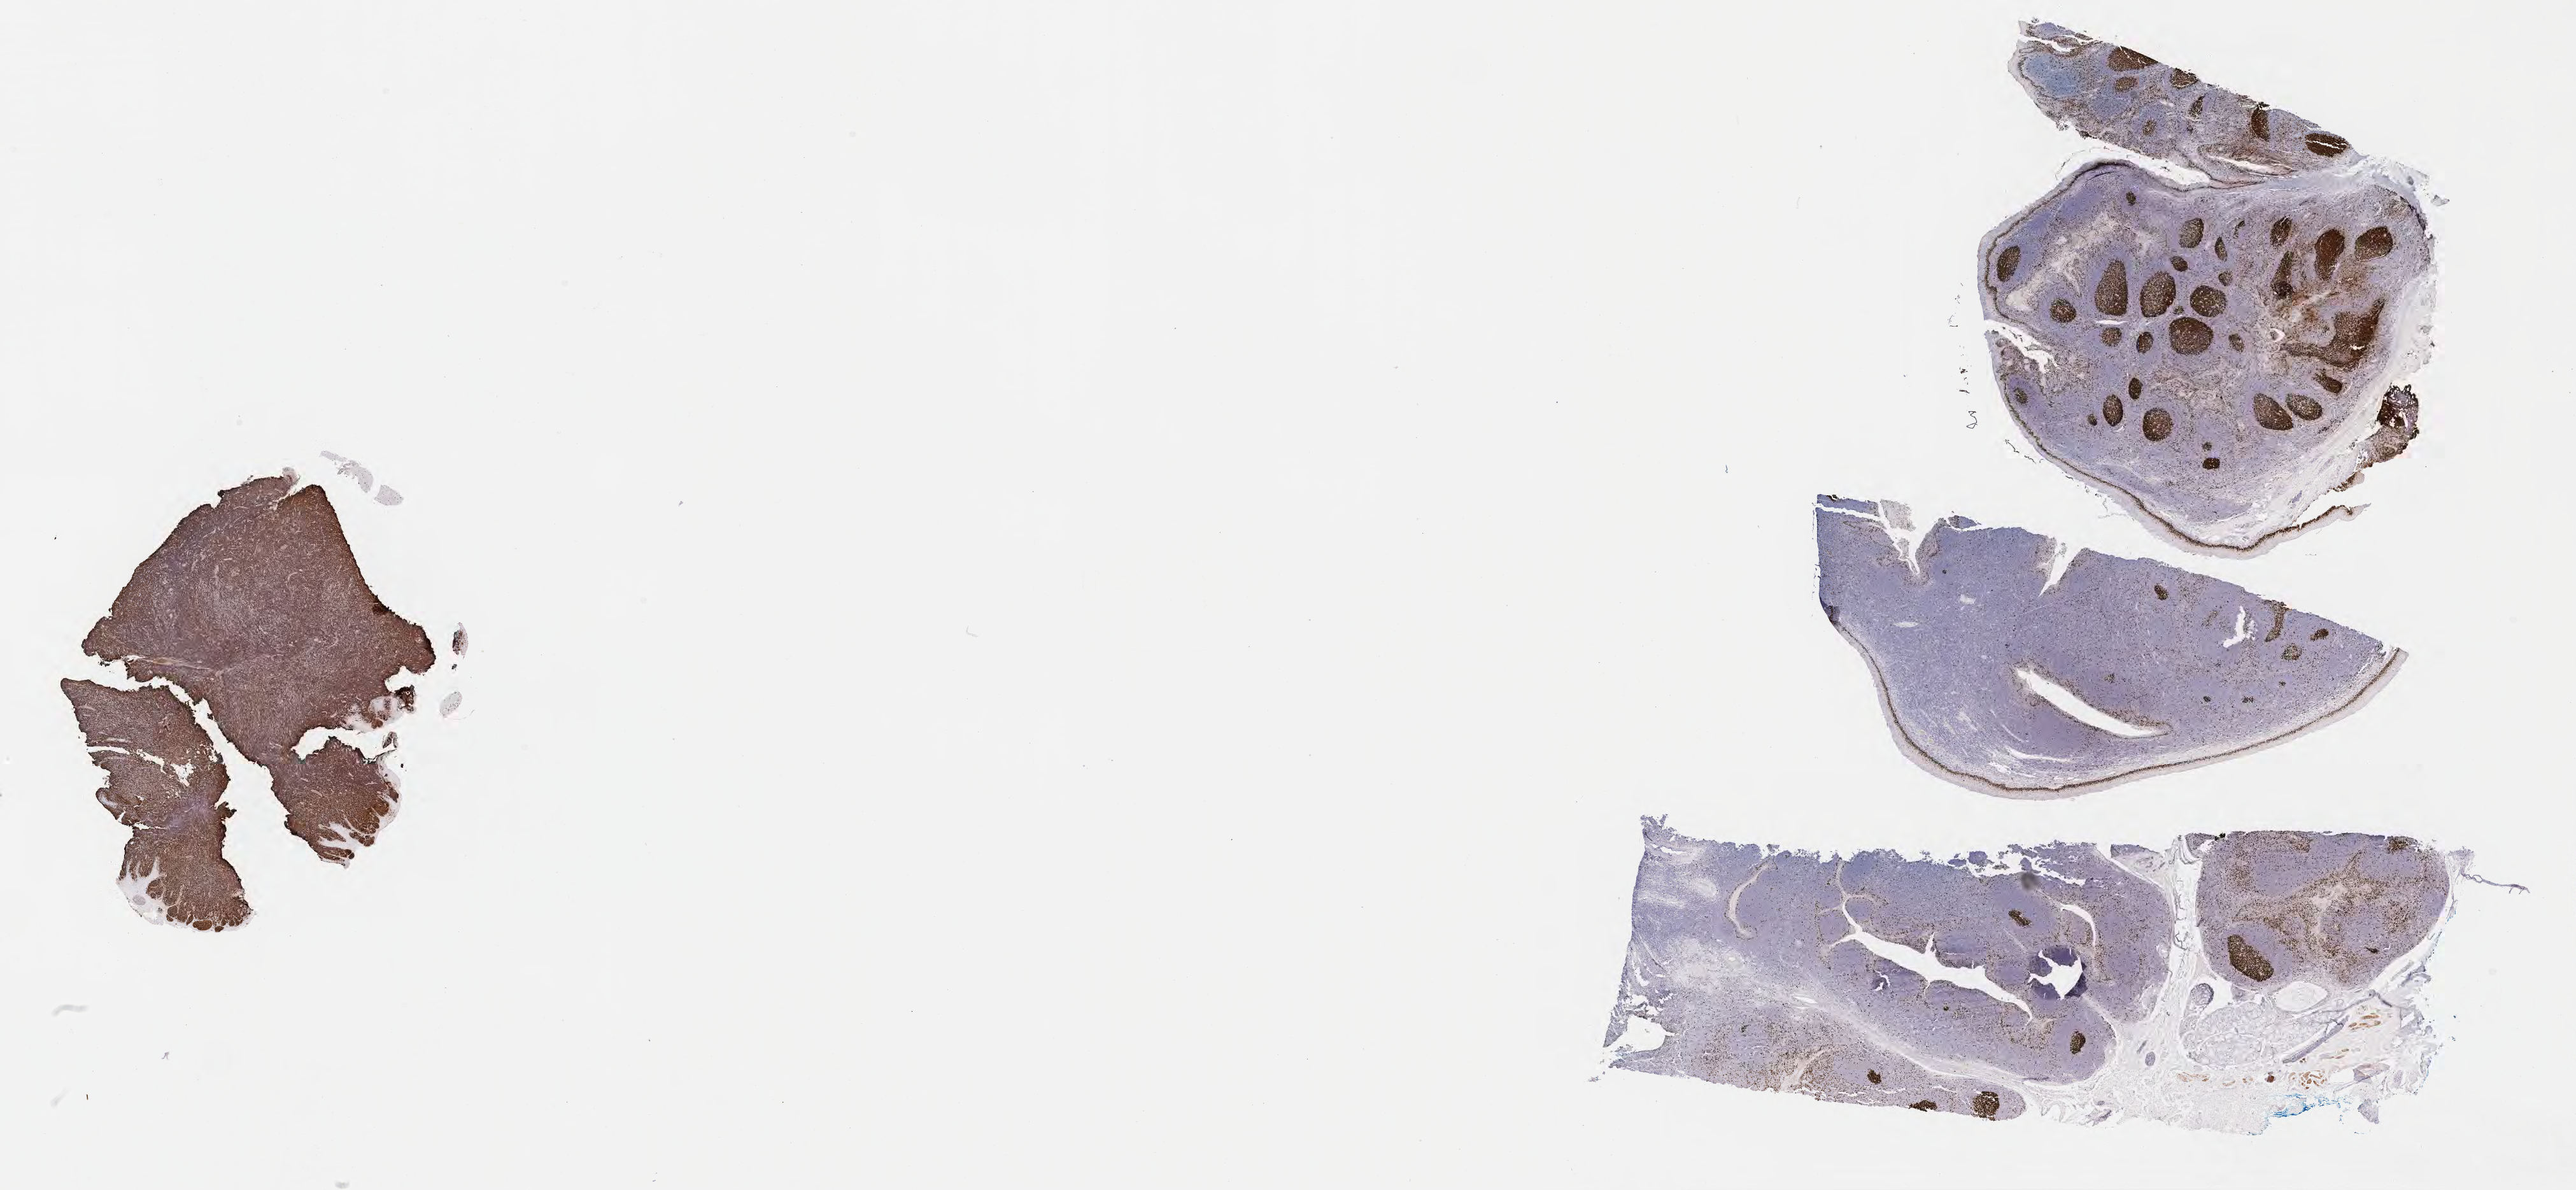
IHC for Ki-67, whole-slide image — a low-resolution overview of the entire scanned area, about 32.7 x 15.1 mm. Tumor tissue. Anatomic site: cranium. Male patient, 11 years old.
Histologic diagnosis: Diffuse large B-cell lymphoma, NOS.